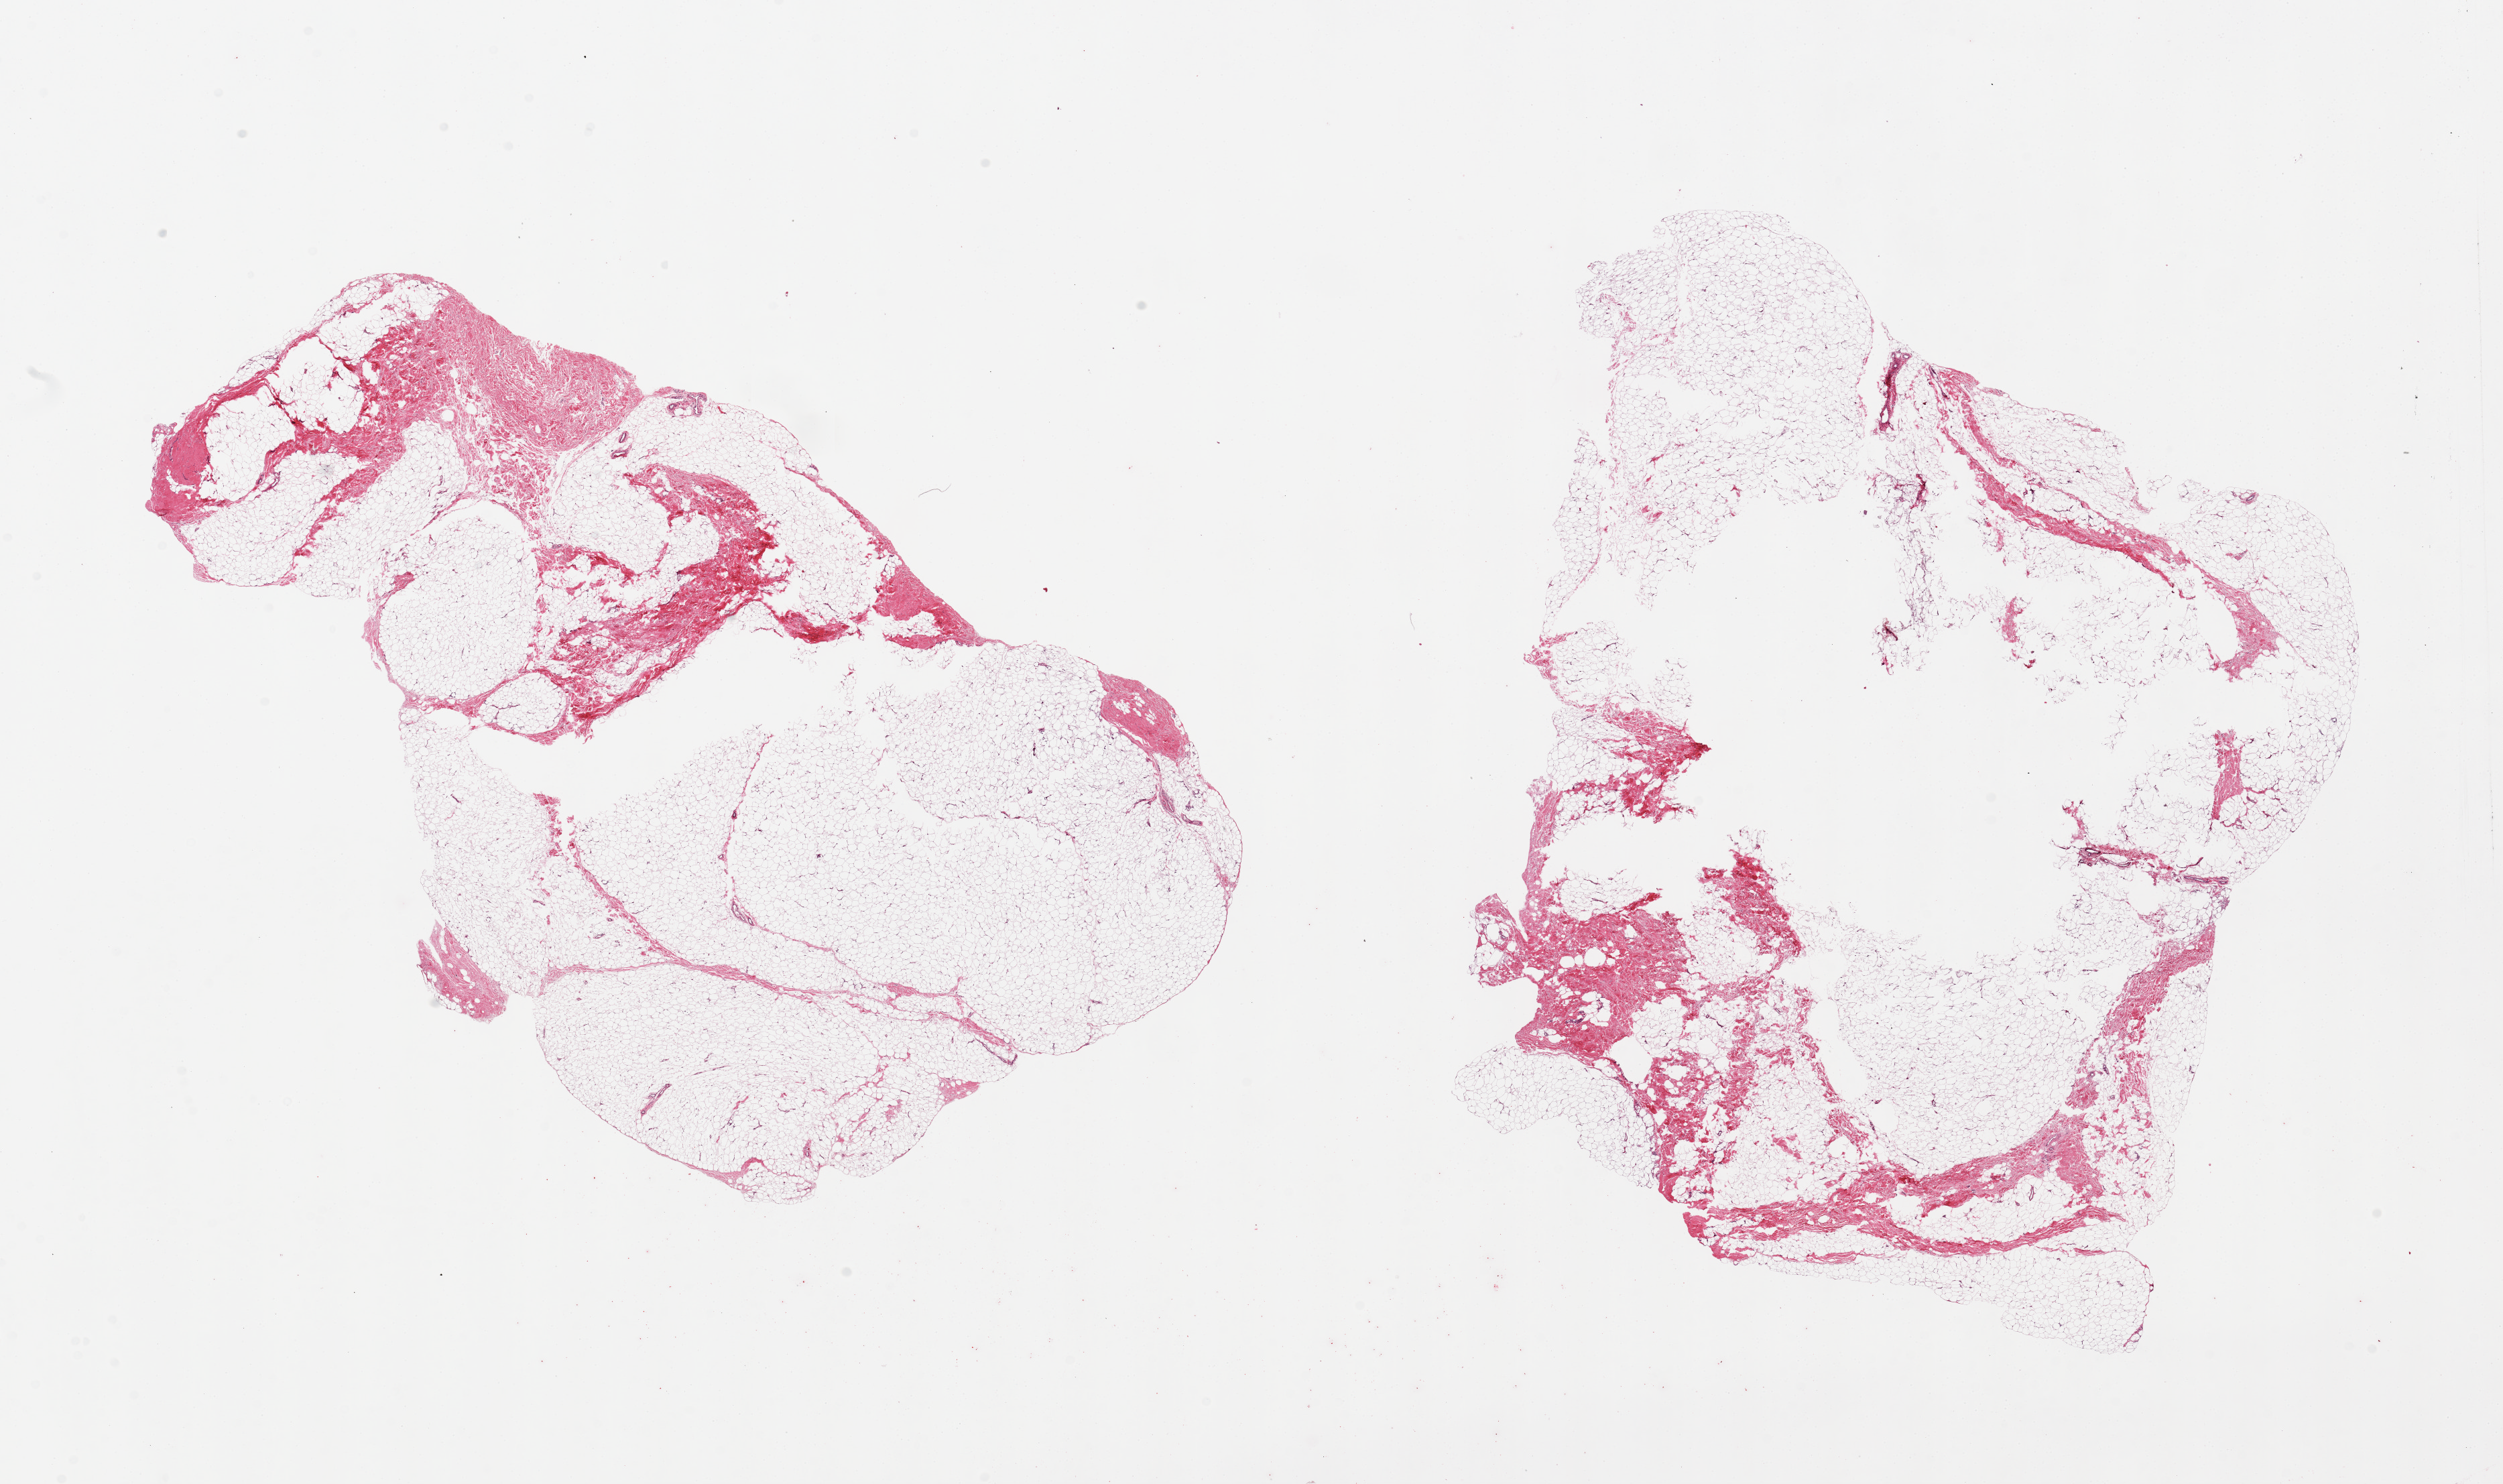
Digitized hematoxylin and eosin (H&E)-stained section — a low-resolution overview of the entire scanned area, about 29.5 x 17.5 mm. PAXgene-fixed, paraffin-embedded tissue. Sampled site (target tissue): breast. Donor tissue sample. Male donor.
* pathologist's review note for this sample: 2 pieces, poorly fixed with central cavity, both with ~10% fibrous tissue, no ductal elements